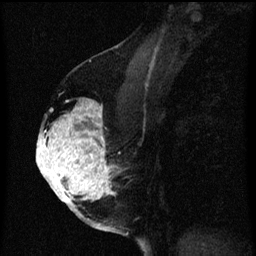
Breast MRI (dynamic contrast-enhanced), one sagittal slice. Dynamic contrast-enhanced series, image 2 of 3 at this slice position (ordered by acquisition). 1.5 T. TE 4.2 ms, TR 8 ms. 2 mm slice thickness. 256 × 256 image matrix, field of view 180 × 180 mm. Patient: female, 56 years.
Annotated regions visible in this slice (semi-automatically segmented with operator editing):
- analysis volume of interest (the breast-tissue region the enhancement analysis was run in; not a lesion): bounding box [x1, y1, x2, y2] px = [40, 100, 121, 205]
- tumour enhancement mask (voxels above the 70 % enhancement threshold inside the analysis volume of interest): [40, 100, 117, 205]